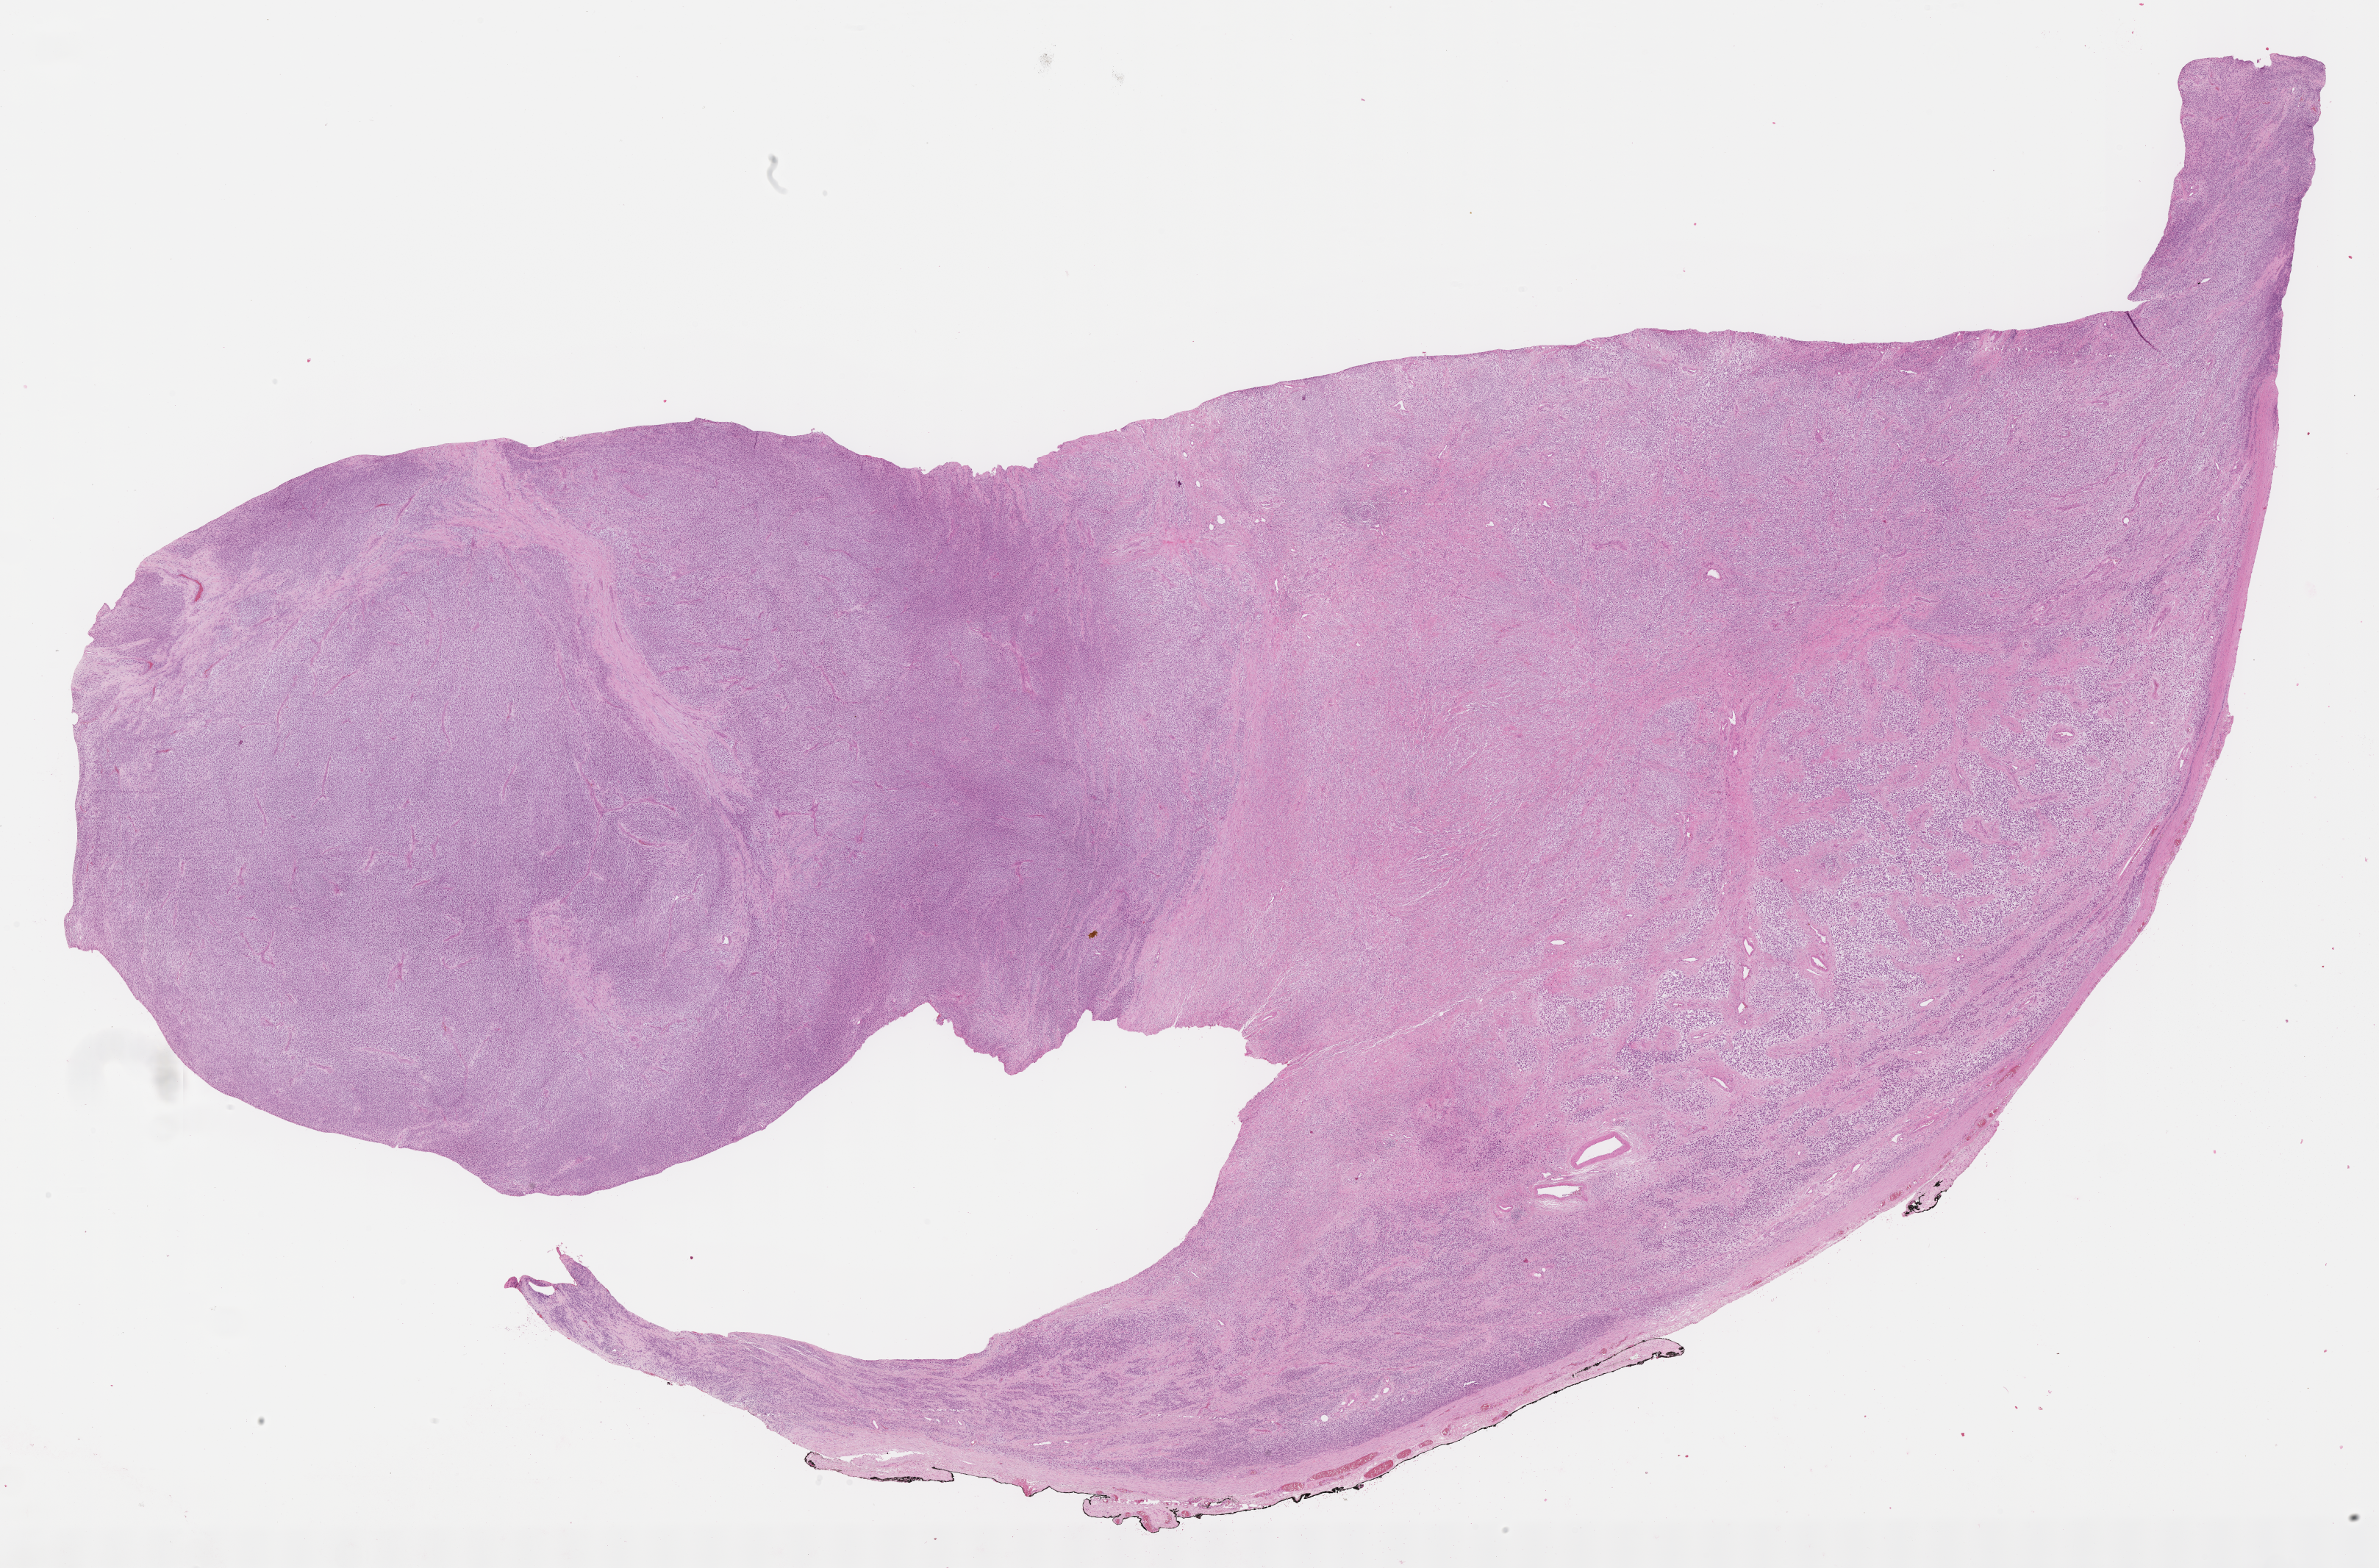
Whole-slide image, hematoxylin and eosin (H&E) stain of tumor tissue, a low-resolution overview of the entire scanned area, about 26.2 x 17.2 mm, formalin-fixed, paraffin-embedded (FFPE) tissue, sample anatomic site: testicle, left. Patient: male, age 4.8 years at diagnosis.
Diagnosis: rhabdomyosarcoma; histological classification: spindle cell rhabdomyosarcoma. Metastatic status at presentation (as recorded): non-metastatic (confirmed). Primary site (case record): testis-paratesticular. Stage (as recorded): 1.